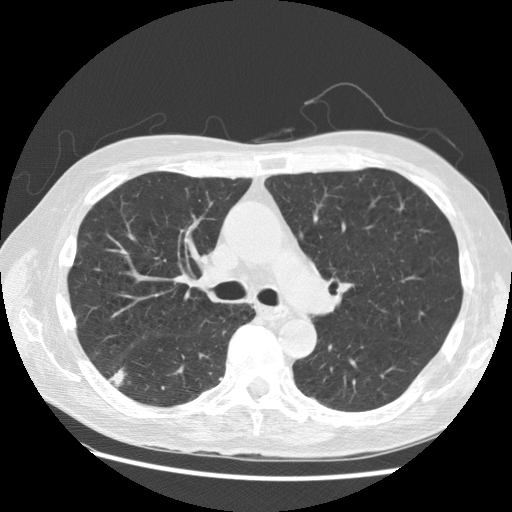
Low-dose screening chest CT, one axial slice; position 102 of 168 along the scan axis; 120 kVp; lung window (W 1500 / L -600 HU); 512 × 512 image matrix, field of view 360 × 360 mm.
Annotated regions visible in this slice (manually delineated by an expert):
- lesion 1 (tumor, lower lobe of right lung): bounding box <113,372,124,384> (left, top, right, bottom; pixels)